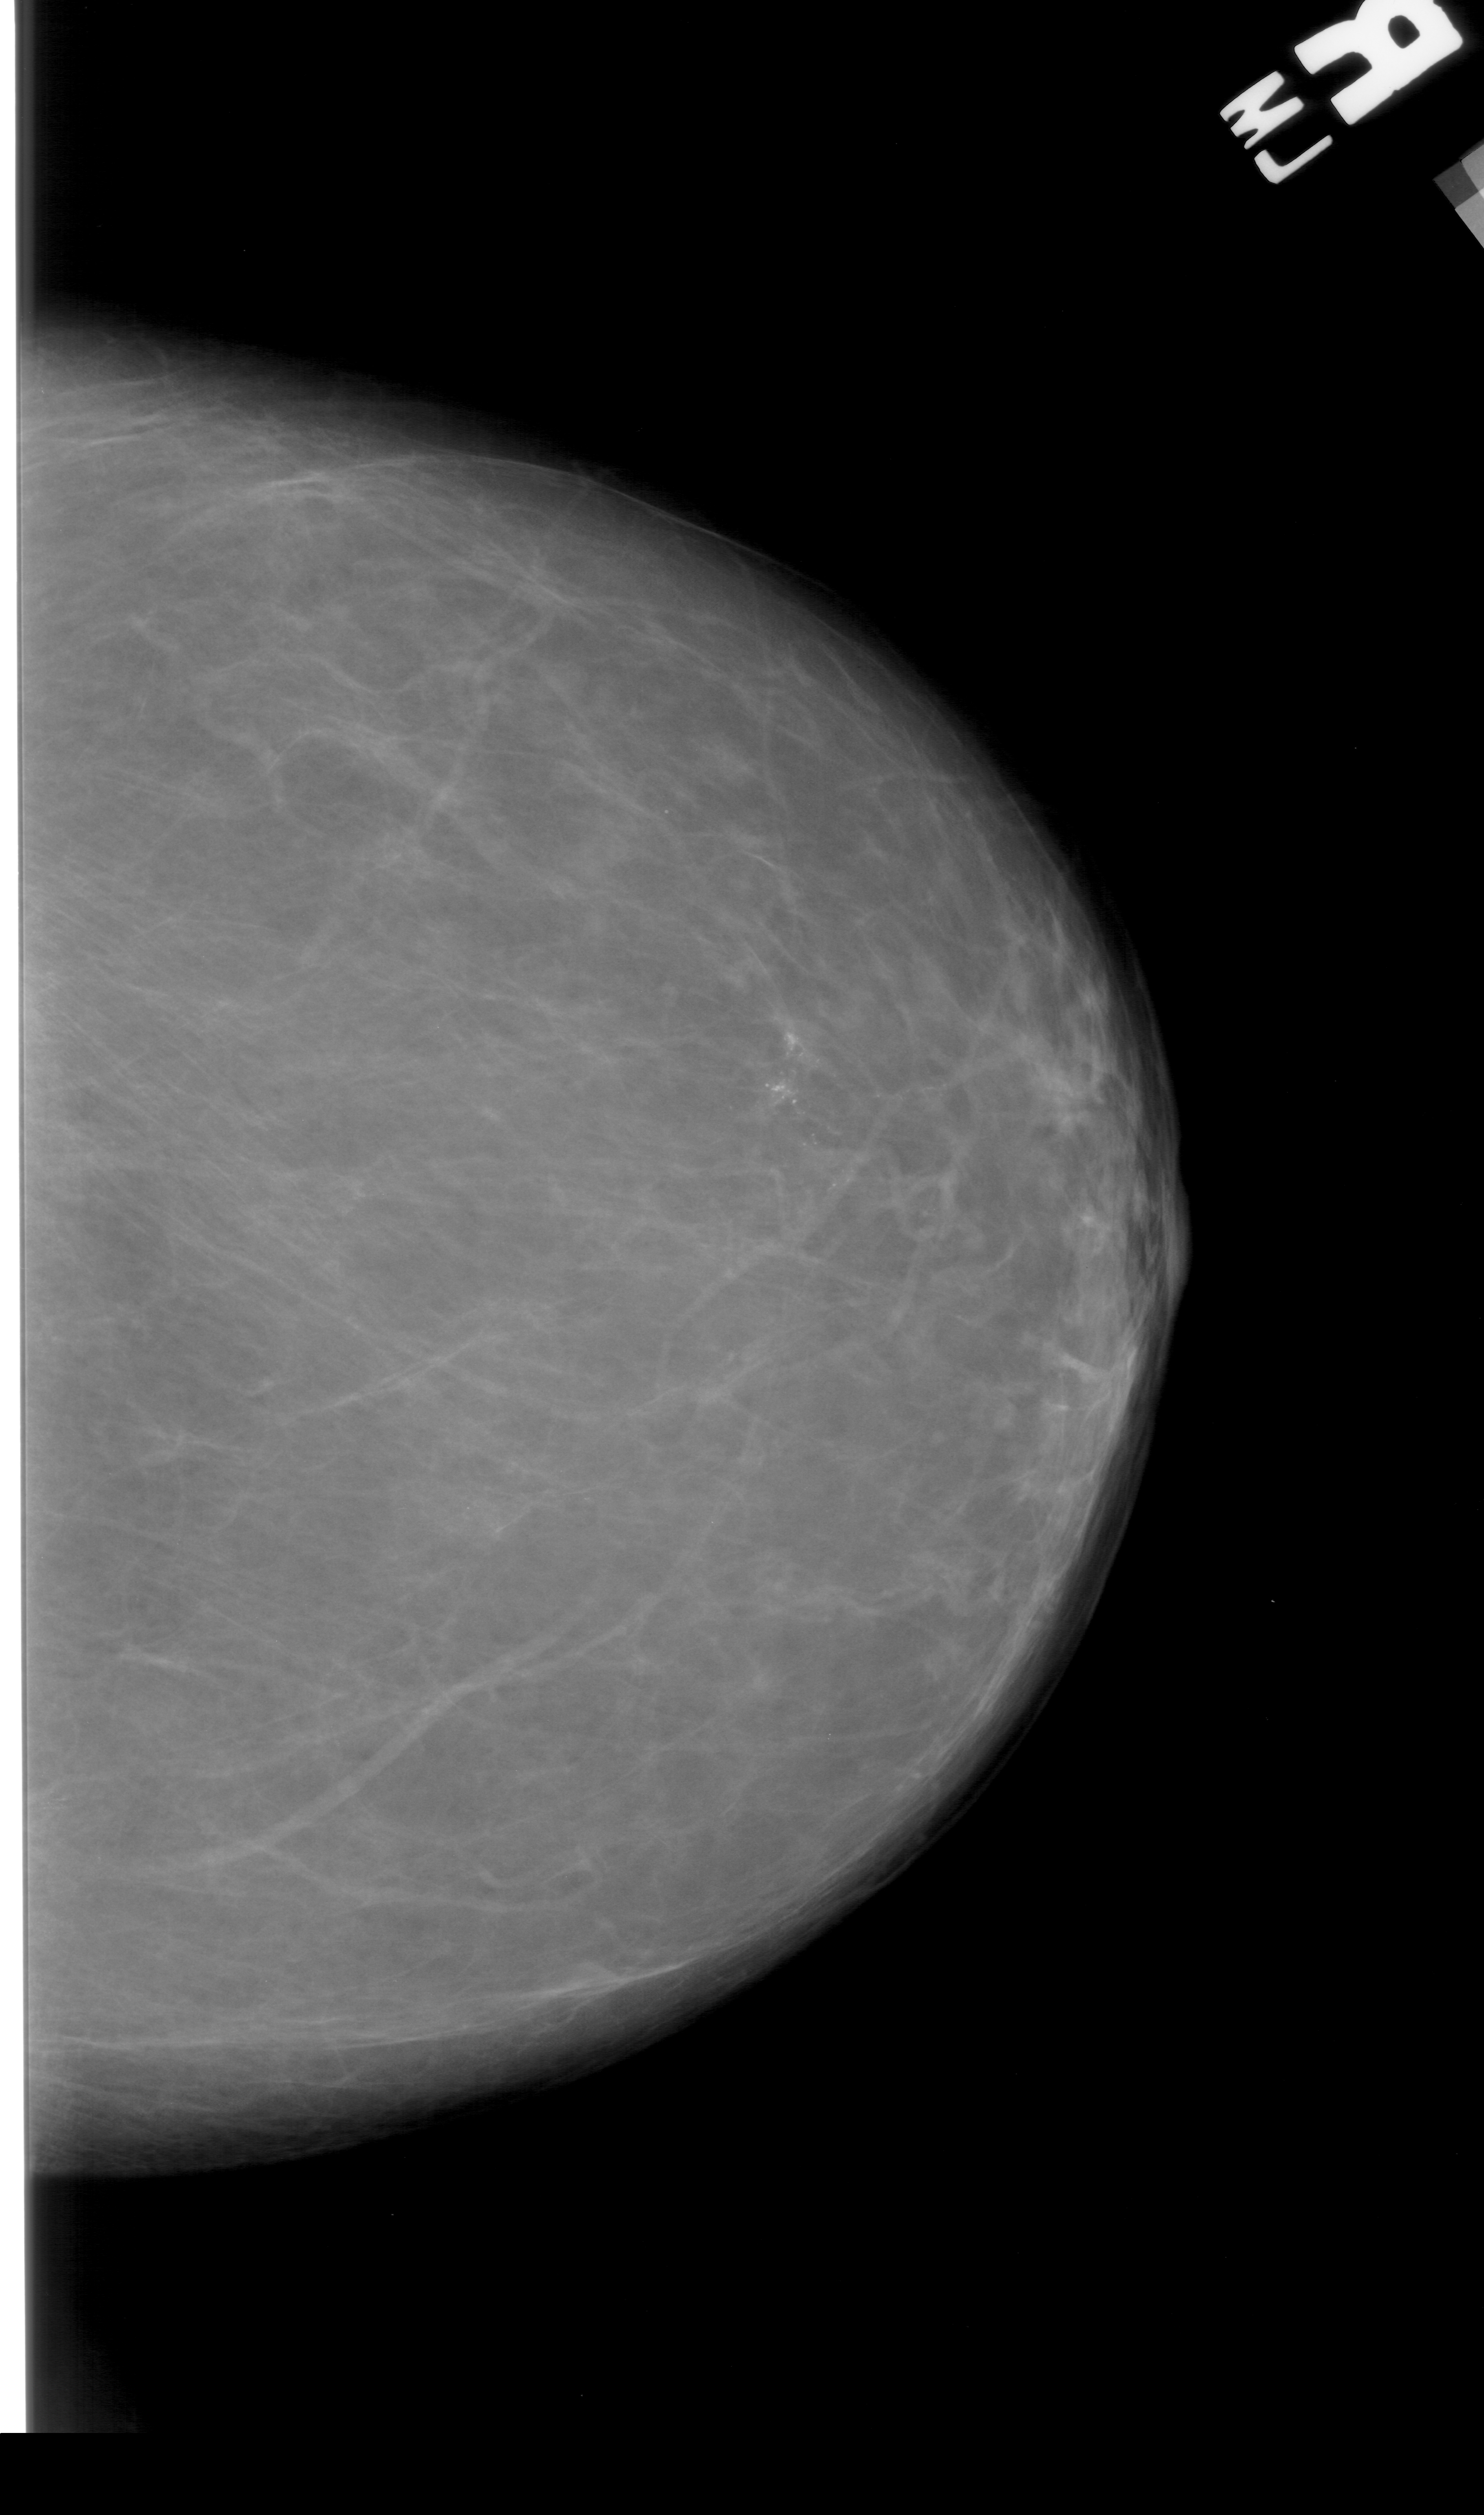
Scanned film-screen mammogram, right breast, CC view, BI-RADS breast density category 2 (scale 1–4).
Finding: calcifications, morphology pleomorphic, distribution segmental; BI-RADS assessment category 4; subtlety rating 4 on a 1 (subtle) to 5 (obvious) scale; pathology (as recorded): malignant.